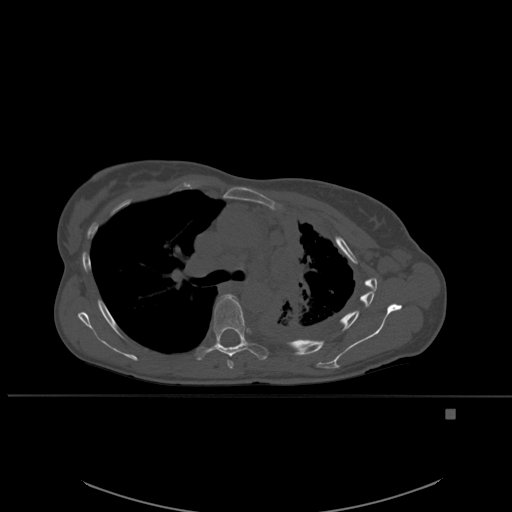
CT including the spine, one axial slice. Position 385 of 537 along the scan axis. Bone window (W 1800 / L 400 HU). 1.5 mm slice thickness. 512 × 512 image matrix, field of view 440 × 440 mm. Female patient, age 45 years. Case-level facts recorded for this patient, not image findings: primary cancer: lung.
Structures marked on this image (semi-automatic segmentation, software-assisted and operator-edited):
- T5 vertebra: bounding box [x1, y1, x2, y2] px = [220, 294, 238, 369]
- T6 vertebra: [196, 294, 268, 367]